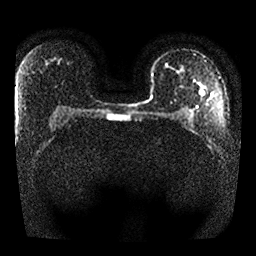
Breast MRI, one axial slice. Slice 16 of 25 in the series (ordered by position). Diffusion-weighted series; image 2 of 4 stored at this slice position (different b-values; order by instance number). 1.5 T. 4 mm slice thickness. 256 × 256 image matrix. Female patient.
Annotated regions visible in this slice (expert manual segmentation):
- tumour on diffusion-weighted imaging: box from (x=176, y=67) to (x=184, y=75) px